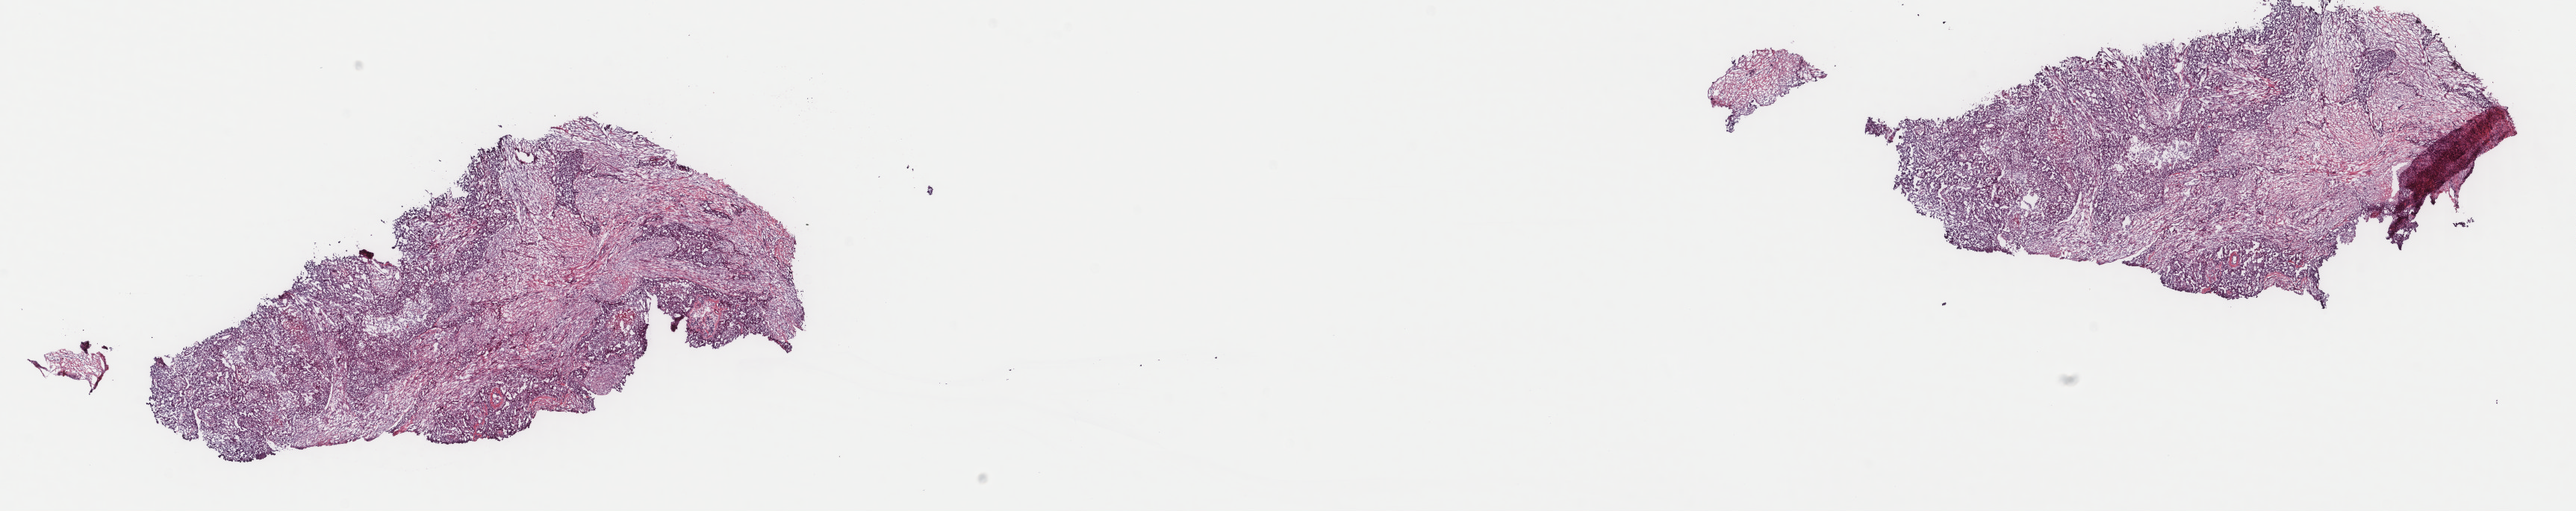
Digitized H&E-stained tissue section (whole slide) — a low-resolution overview of the entire scanned area, about 27.4 x 5.4 mm (from a 40x scan), frozen section from the top of the tissue portion, sample: primary tumour, mesothelium. Patient: female, age at initial diagnosis 55 years. Pathologist review of this section (percent, as recorded): tumour cells 100%, tumour nuclei 80%, normal cells 0%, stromal cells 0%, necrosis 0%. Infiltration values recorded for this section: lymphocyte infiltration 1%, monocyte infiltration 0%, neutrophil infiltration 0%.
Laterality: left. AJCC pathologic stage: III. Histologic diagnosis: Epithelioid mesothelioma, malignant (pleura, NOS).